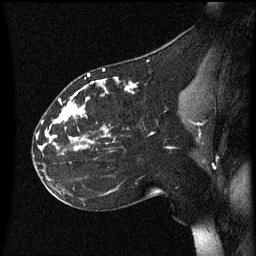
Breast MRI (dynamic contrast-enhanced), one sagittal slice. Slice 30 of 60 in the series (ordered by position). Dynamic contrast-enhanced series, image 2 of 3 at this slice position (ordered by acquisition). 1.5 T. TE 4.2 ms, TR 8.4 ms. 2.2 mm slice thickness. 256 × 256 image matrix, field of view 200 × 200 mm. Patient: female, 35 years. Case-level facts recorded for this patient, not image findings: setting: breast cancer imaged before/during neoadjuvant chemotherapy; receptor status: HER2-positive.
Annotated regions visible in this slice (semi-automatic segmentation, software-assisted and operator-edited):
- analysis volume of interest (the breast-tissue region the enhancement analysis was run in; not a lesion): box from (x=33, y=72) to (x=172, y=173) px
- tumour enhancement mask (voxels above the 70 % enhancement threshold inside the analysis volume of interest): (x=39, y=74)–(x=137, y=151)